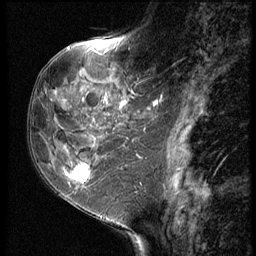
Breast MRI (dynamic contrast-enhanced), one sagittal slice; slice 24 of 62 in the series (ordered by position); 3 images stored at this slice position (order not interpretable as contrast timing); 1.5 T; TE 4.2 ms, TR 9 ms; 2.5 mm slice thickness; 256 × 256 image matrix, field of view 180 × 180 mm. Female patient, age 50 years. Case-level facts recorded for this patient, not image findings: setting: breast cancer imaged before/during neoadjuvant chemotherapy; receptor status: HR-positive, HER2-negative.
Structures marked on this image (semi-automatic segmentation, software-assisted and operator-edited):
- analysis volume of interest (the breast-tissue region the enhancement analysis was run in; not a lesion): bounding box <32,91,118,209> (left, top, right, bottom; pixels)
- tumour enhancement mask (voxels above the 140 % enhancement threshold inside the analysis volume of interest): <68,161,92,180>